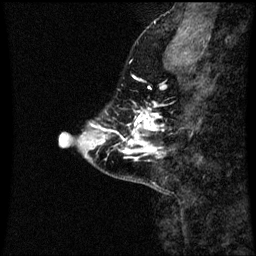
Breast MRI (dynamic contrast-enhanced), one sagittal slice; dynamic contrast-enhanced series, image 2 of 3 at this slice position (ordered by acquisition); 1.5 T; TE 4.2 ms, TR 8.9 ms; 256 × 256 image matrix, field of view 200 × 200 mm. Patient: female, 43 years. Case-level facts recorded for this patient, not image findings: setting: breast cancer imaged before/during neoadjuvant chemotherapy; receptor status: HR-positive, HER2-negative.
Structures marked on this image (semi-automatic segmentation, software-assisted and operator-edited):
- analysis volume of interest (the breast-tissue region the enhancement analysis was run in; not a lesion): bounding box [x1, y1, x2, y2] px = [117, 102, 164, 161]
- tumour enhancement mask (voxels above the 70 % enhancement threshold inside the analysis volume of interest): [123, 114, 161, 161]